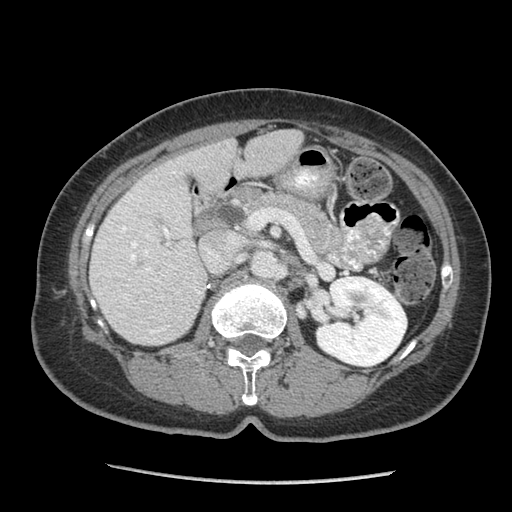
Contrast-enhanced abdominal CT (liver protocol), one axial slice; position 38 of 105 along the scan axis; reconstruction kernel STANDARD; 140 kVp; soft-tissue window (W 400 / L 40 HU); 2.5 mm slice thickness; 512 × 512 image matrix. From the clinical record (not read from this slice): diagnosis: hepatocellular carcinoma (patient treated with transarterial chemoembolisation; whether this scan precedes or follows treatment is not stated here); TNM stage (as recorded): Stage-I; Child-Pugh class: A; tumour differentiation: moderately differentiated; tumour nodularity: uninodular.
Annotated regions visible in this slice (semi-automatic segmentation, software-assisted and operator-edited):
- liver parenchyma outside the tumour (the mass and vessels are separate outlines, so this box may not span the whole liver): box from (x=90, y=130) to (x=303, y=344) px
- liver vessels: (x=98, y=171)–(x=202, y=334)